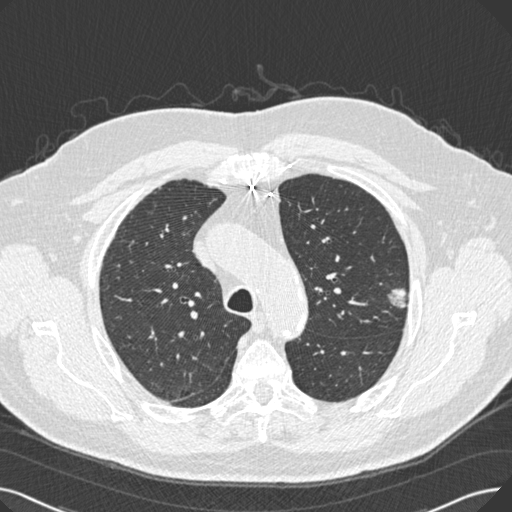
Low-dose screening chest CT, one axial slice. Position 195 of 269 along the scan axis. Reconstruction kernel B30f. Lung window (W 1500 / L -600 HU). 512 × 512 image matrix, field of view 370 × 370 mm.
Structures marked on this image (expert manual segmentation):
- lesion 1 (tumor, upper lobe of left lung): bounding box (x1, y1, x2, y2) in pixels: (388, 289, 407, 308)